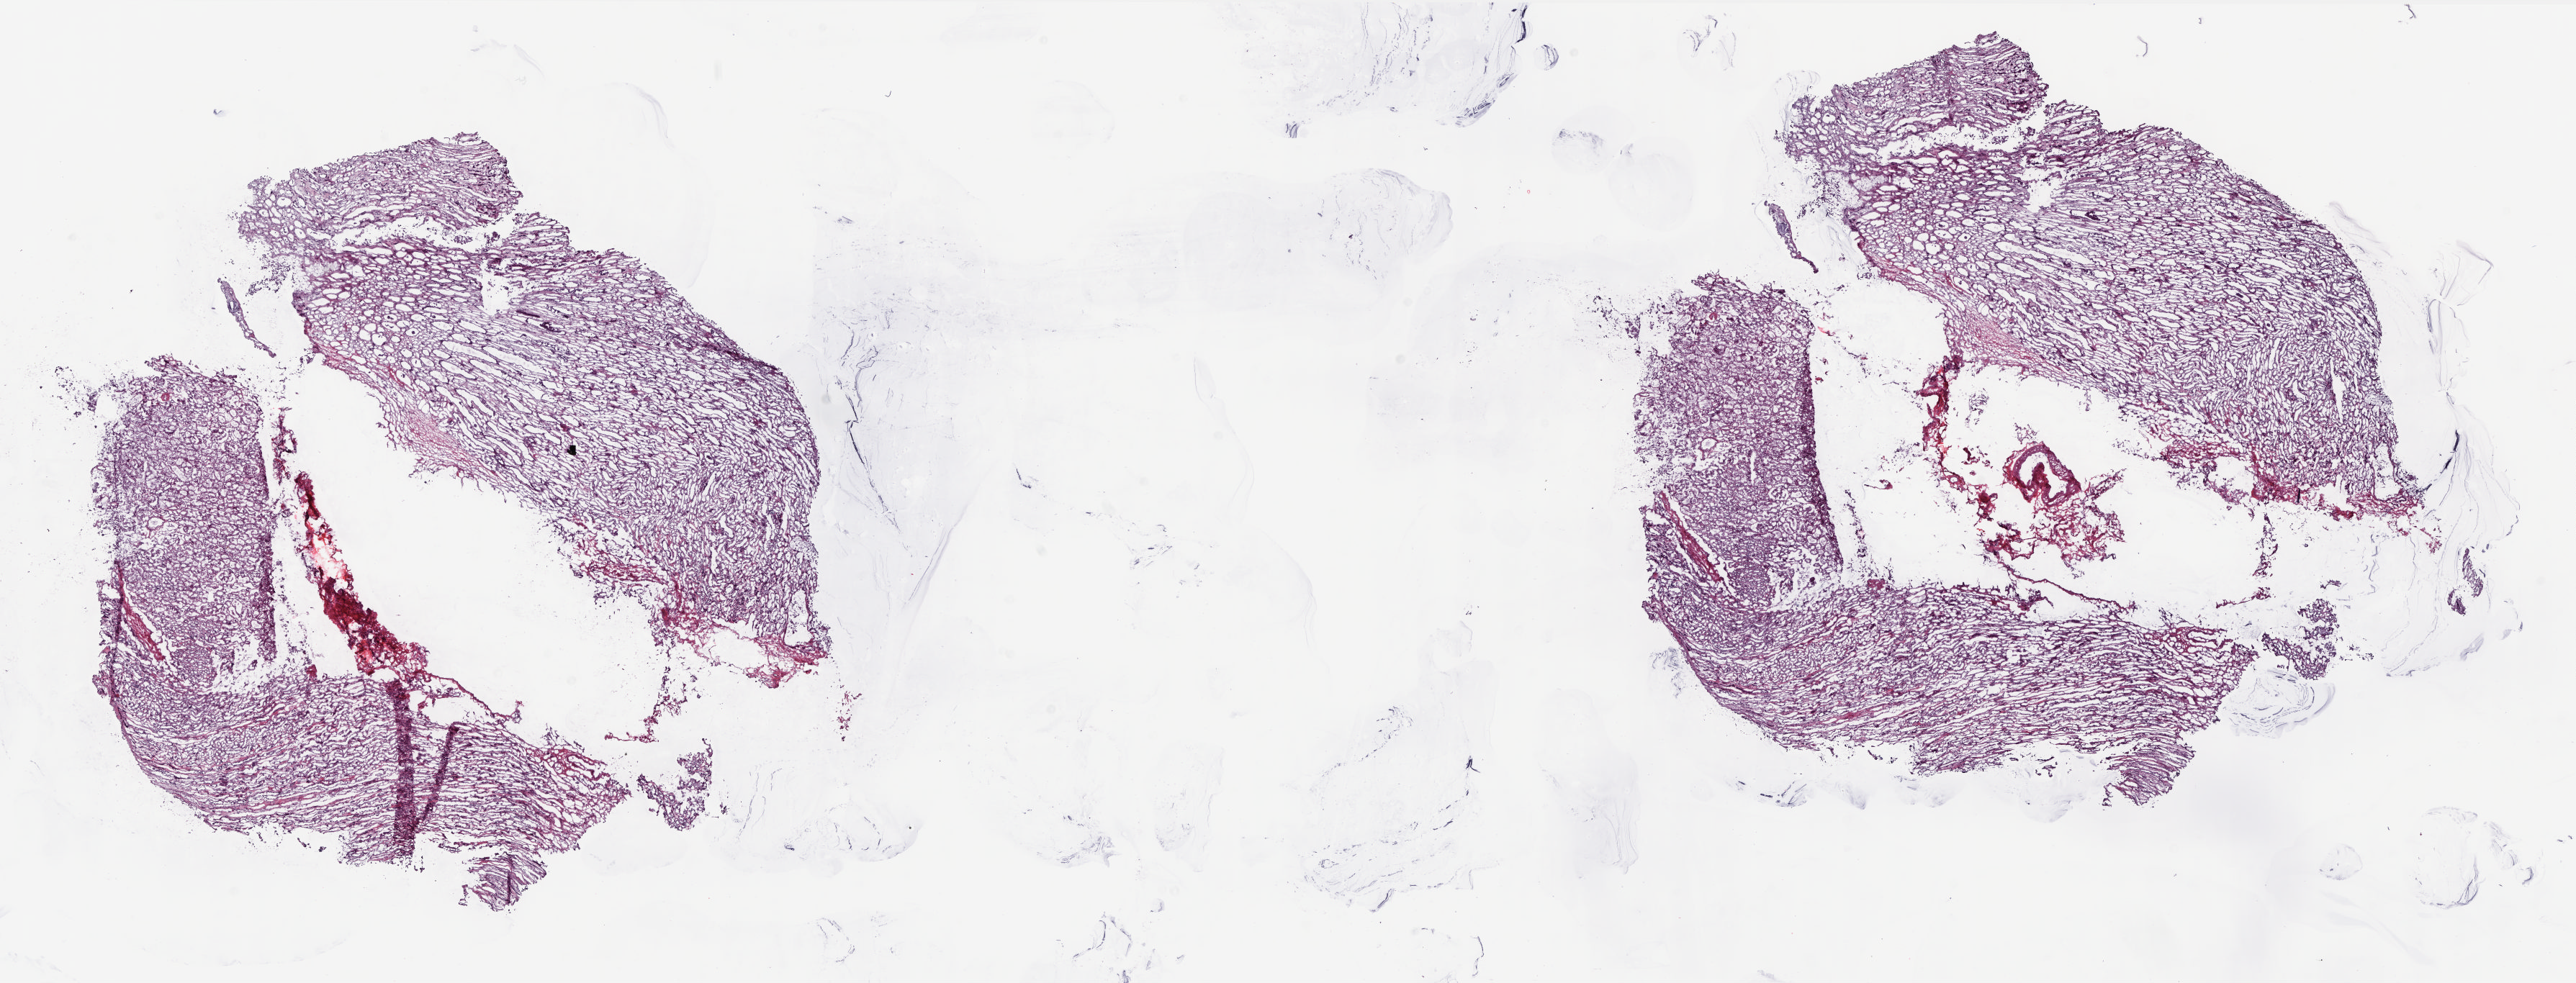
Digitized Hematoxylin and eosin (H&E) stained tissue section (whole slide) — a low-resolution overview of the entire scanned area, about 28.9 x 11.0 mm (slide scanned at 20x), frozen section from the top of the tissue portion, kidney, solid tissue normal (non-tumour tissue) sample. Male, age 51 years at initial diagnosis. Slide review estimates, as recorded: tumour cells 0%, tumour nuclei 0%, normal cells 100%, stromal cells 0%, necrosis 0%. Inflammatory infiltration, as recorded: lymphocyte infiltration 0%, monocyte infiltration 0%, neutrophil infiltration 0%.
- this section: solid tissue normal (non-tumour) sample from the same patient
- patient diagnosis: Papillary adenocarcinoma, NOS